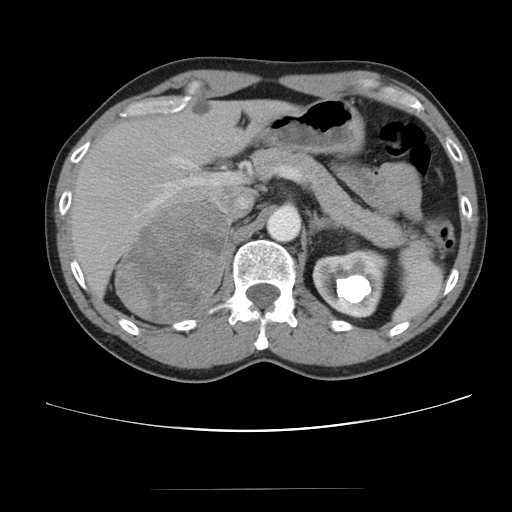
Contrast-enhanced abdominal CT, one axial slice. Position 64 of 80 along the scan axis. Reconstruction kernel STANDARD. 120 kVp. Intravenous contrast given. Soft-tissue window (W 400 / L 40 HU). 5 mm slice thickness. 512 × 512 image matrix. Patient: male, 61 years. Case-level facts recorded for this patient, not image findings: diagnosis: adrenocortical carcinoma; tumour side: right adrenal; tumour size at pathology: 11.1 cm; Ki-67 index: 32 %; stage (as recorded): 2.
Outlined on this slice (semi-automatically segmented with operator editing):
- mass: bounding box (x1, y1, x2, y2) in pixels: (116, 205, 226, 322)